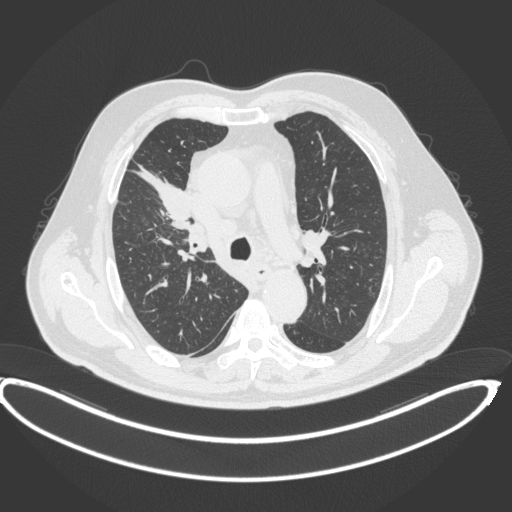
Chest CT, one axial slice; position 277 of 395 along the scan axis; reconstruction kernel B31f; 120 kVp; lung window (W 1500 / L -600 HU); 512 × 512 image matrix, field of view 448 × 448 mm. Patient: male, 62 years. From the clinical record (not read from this slice): clinical TNM (as recorded): T1c N3 M1c.
Annotated regions visible in this slice (bounding box drawn by a radiologist):
- lung tumour (recorded histology: adenocarcinoma): bounding box (x1, y1, x2, y2) in pixels: (133, 164, 191, 223)